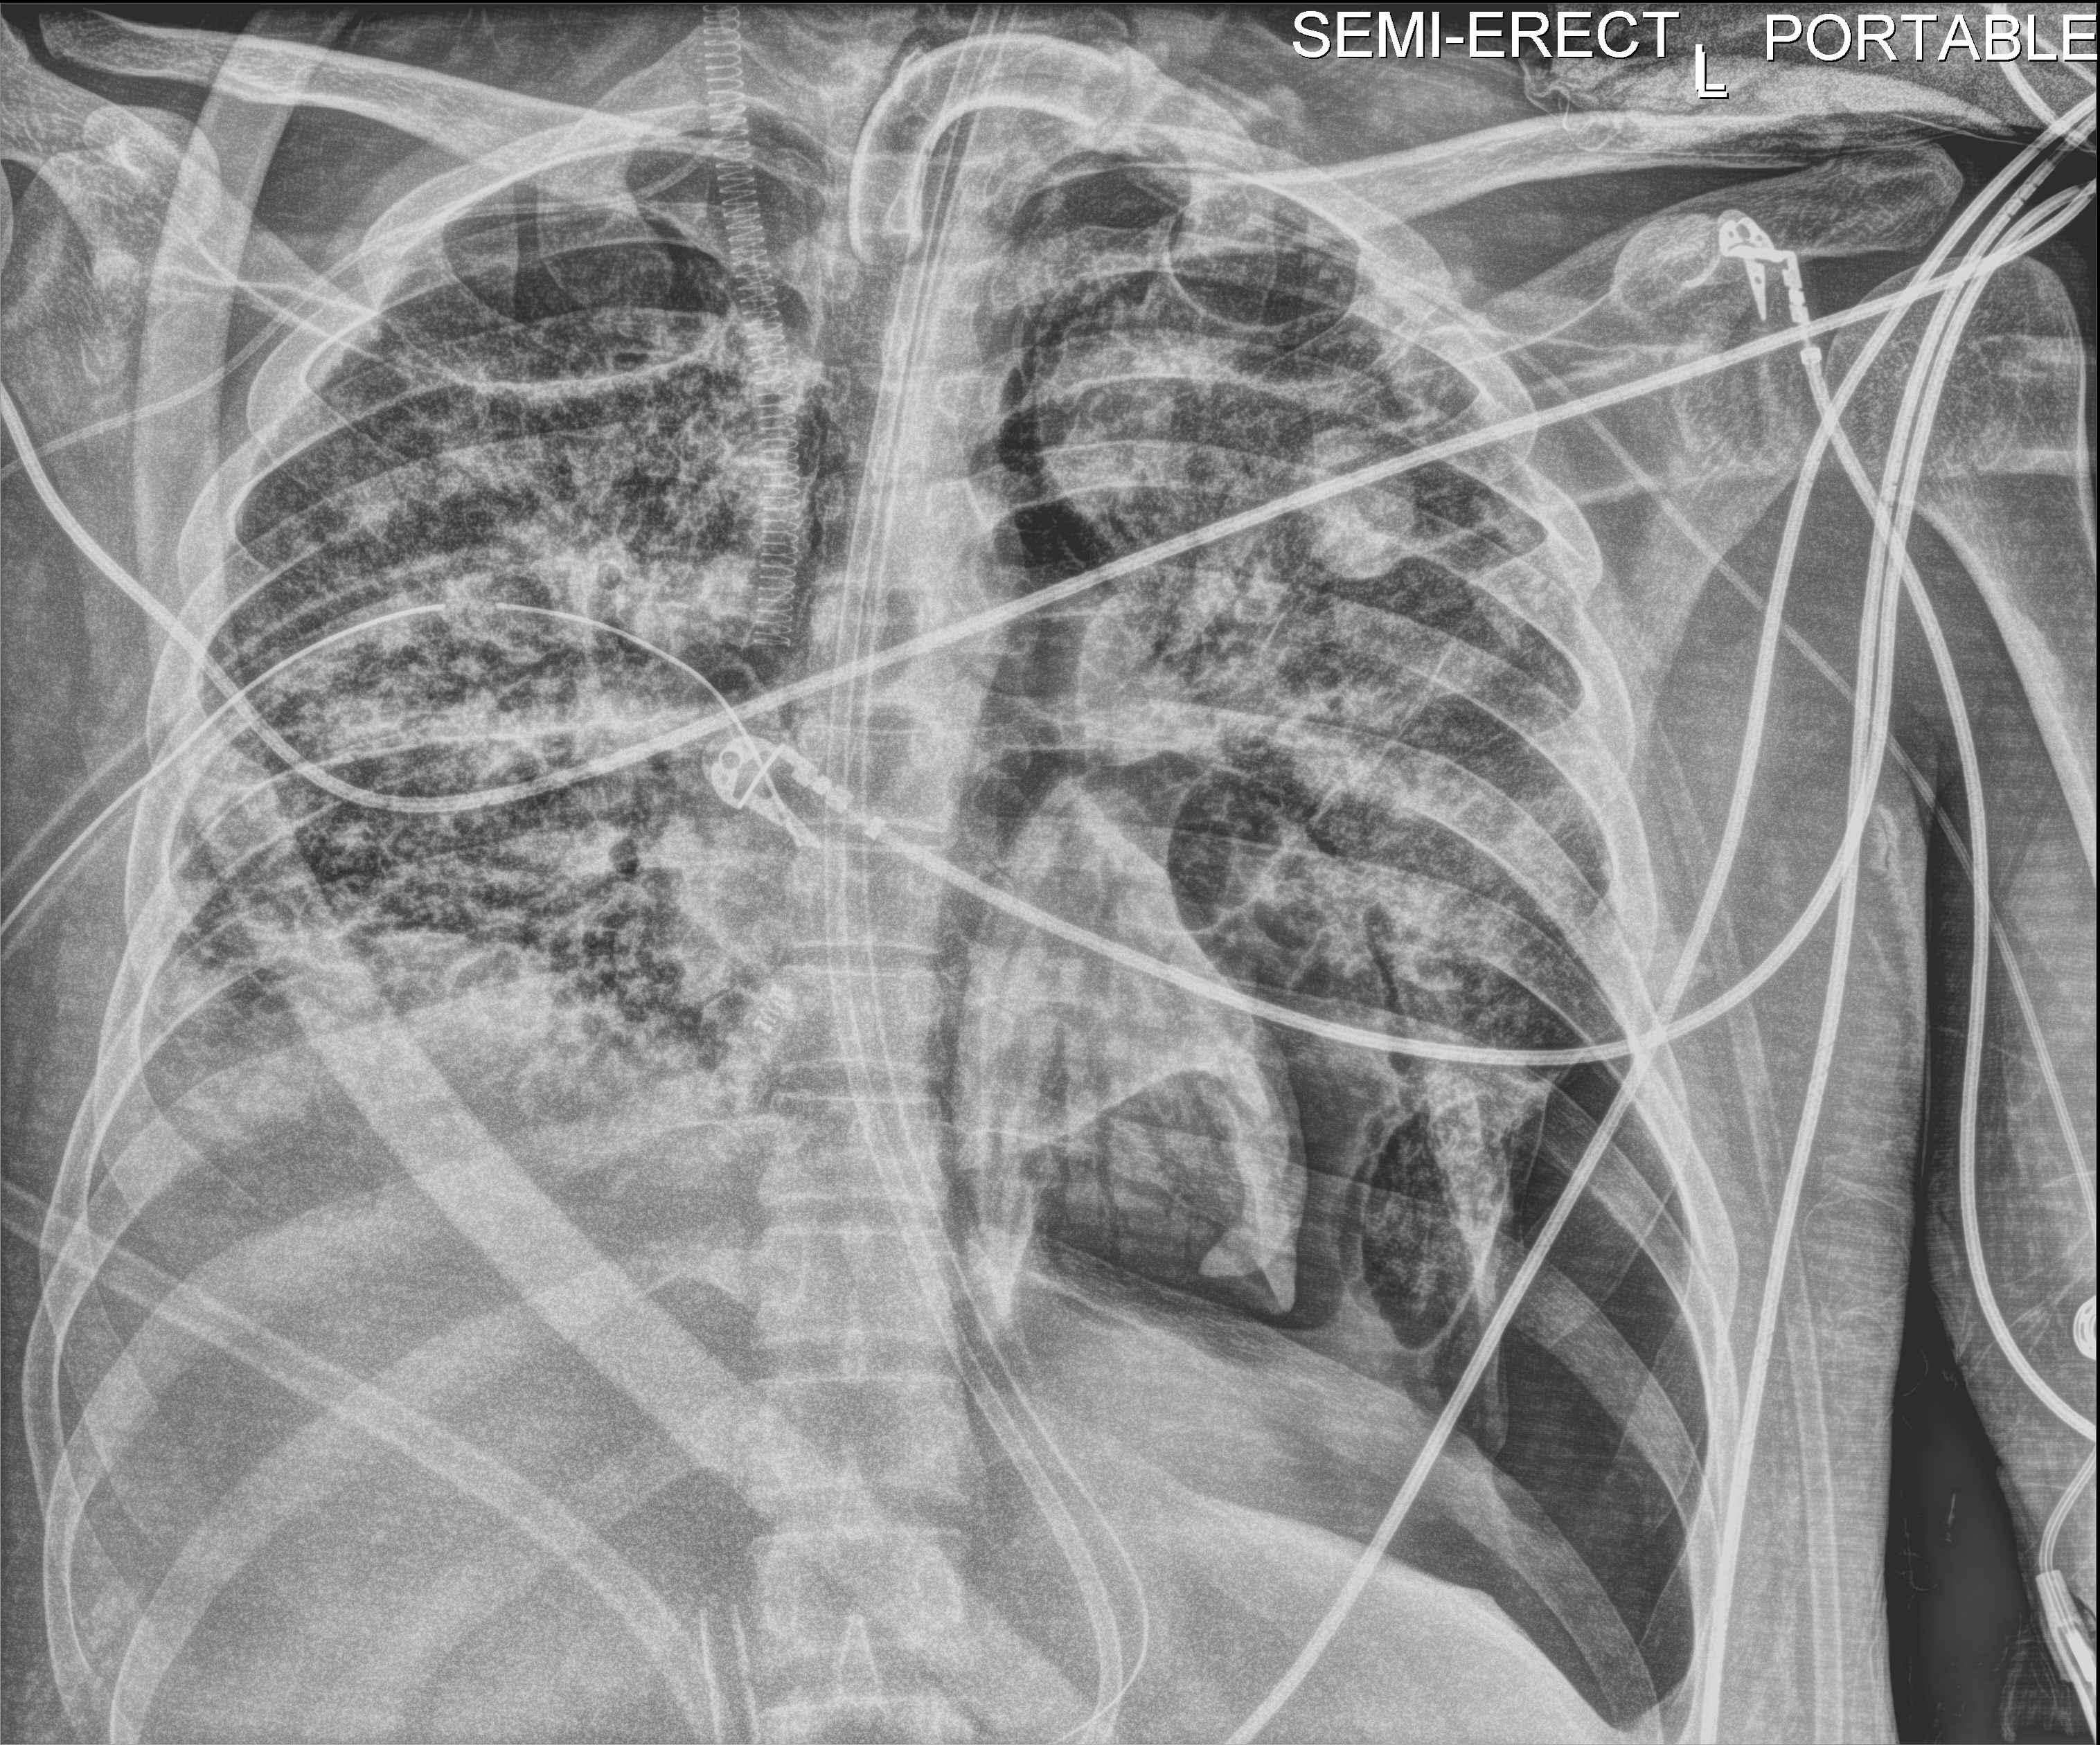
Portable chest radiograph; anteroposterior (AP) projection. Adult patient hospitalised with COVID-19, age 18–59 years.
From the hospital-stay record, not from the radiograph (when in the stay this image was taken is not recorded):
- chronic kidney disease (admission record): no
- admitted to intensive care during this hospital stay: yes
- mechanically ventilated during this hospital stay: yes